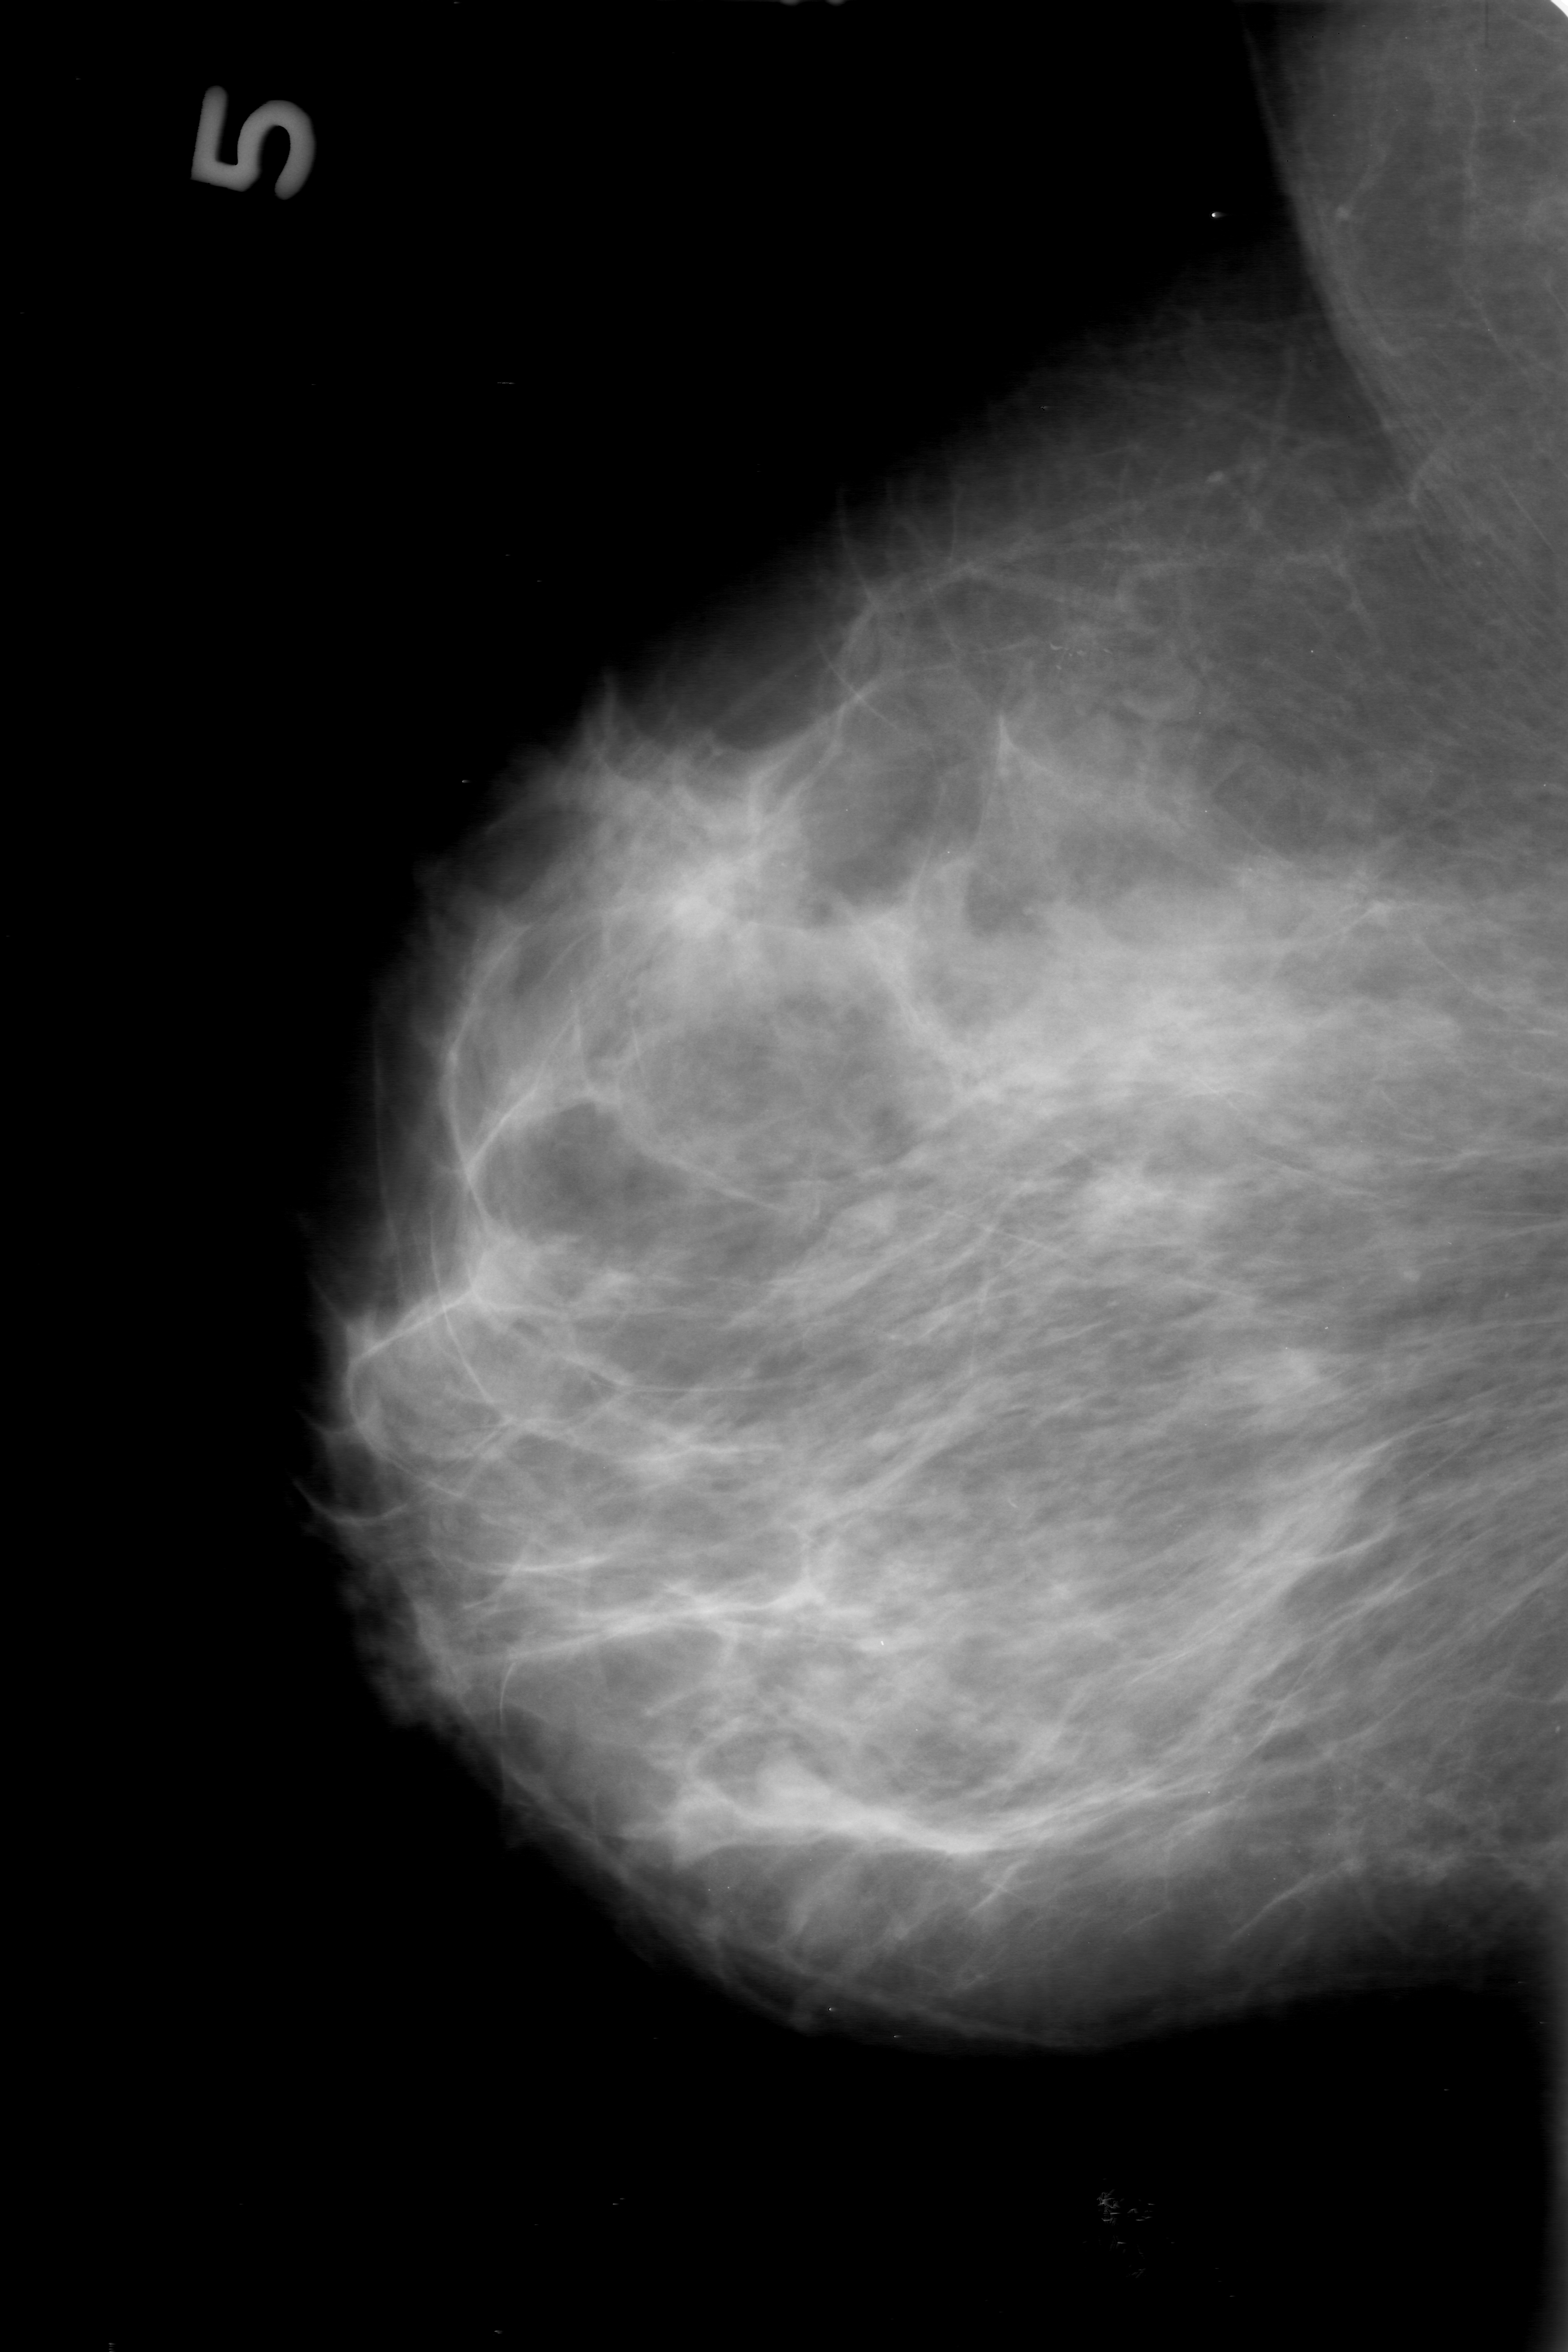
Digitized screen-film mammogram, right breast, MLO view.
Radiologist-marked abnormalities on this image: calcifications, morphology punctate / amorphous, distribution clustered; BI-RADS assessment category 0 (incomplete: needs additional imaging); subtlety rating 2 on a 1 (subtle) to 5 (obvious) scale; pathology result (as recorded, not read from the image): benign.